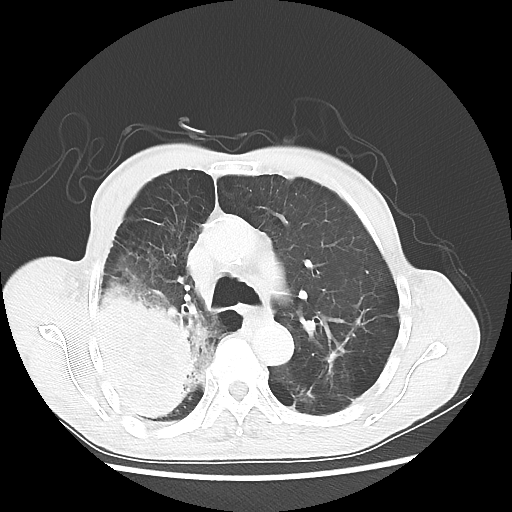
Chest CT, one axial slice. Slice 36 of 58 in the series (ordered by position). Lung window (W 1500 / L -600 HU). 5 mm slice thickness. 512 × 512 image matrix. Male patient, age 75 years. Case-level facts recorded for this patient, not image findings: clinical TNM (as recorded): T4 N1 M1.
Outlined on this slice (bounding box drawn by a radiologist):
- lung tumour (recorded histology: adenocarcinoma): bounding box <93,274,212,420> (left, top, right, bottom; pixels)